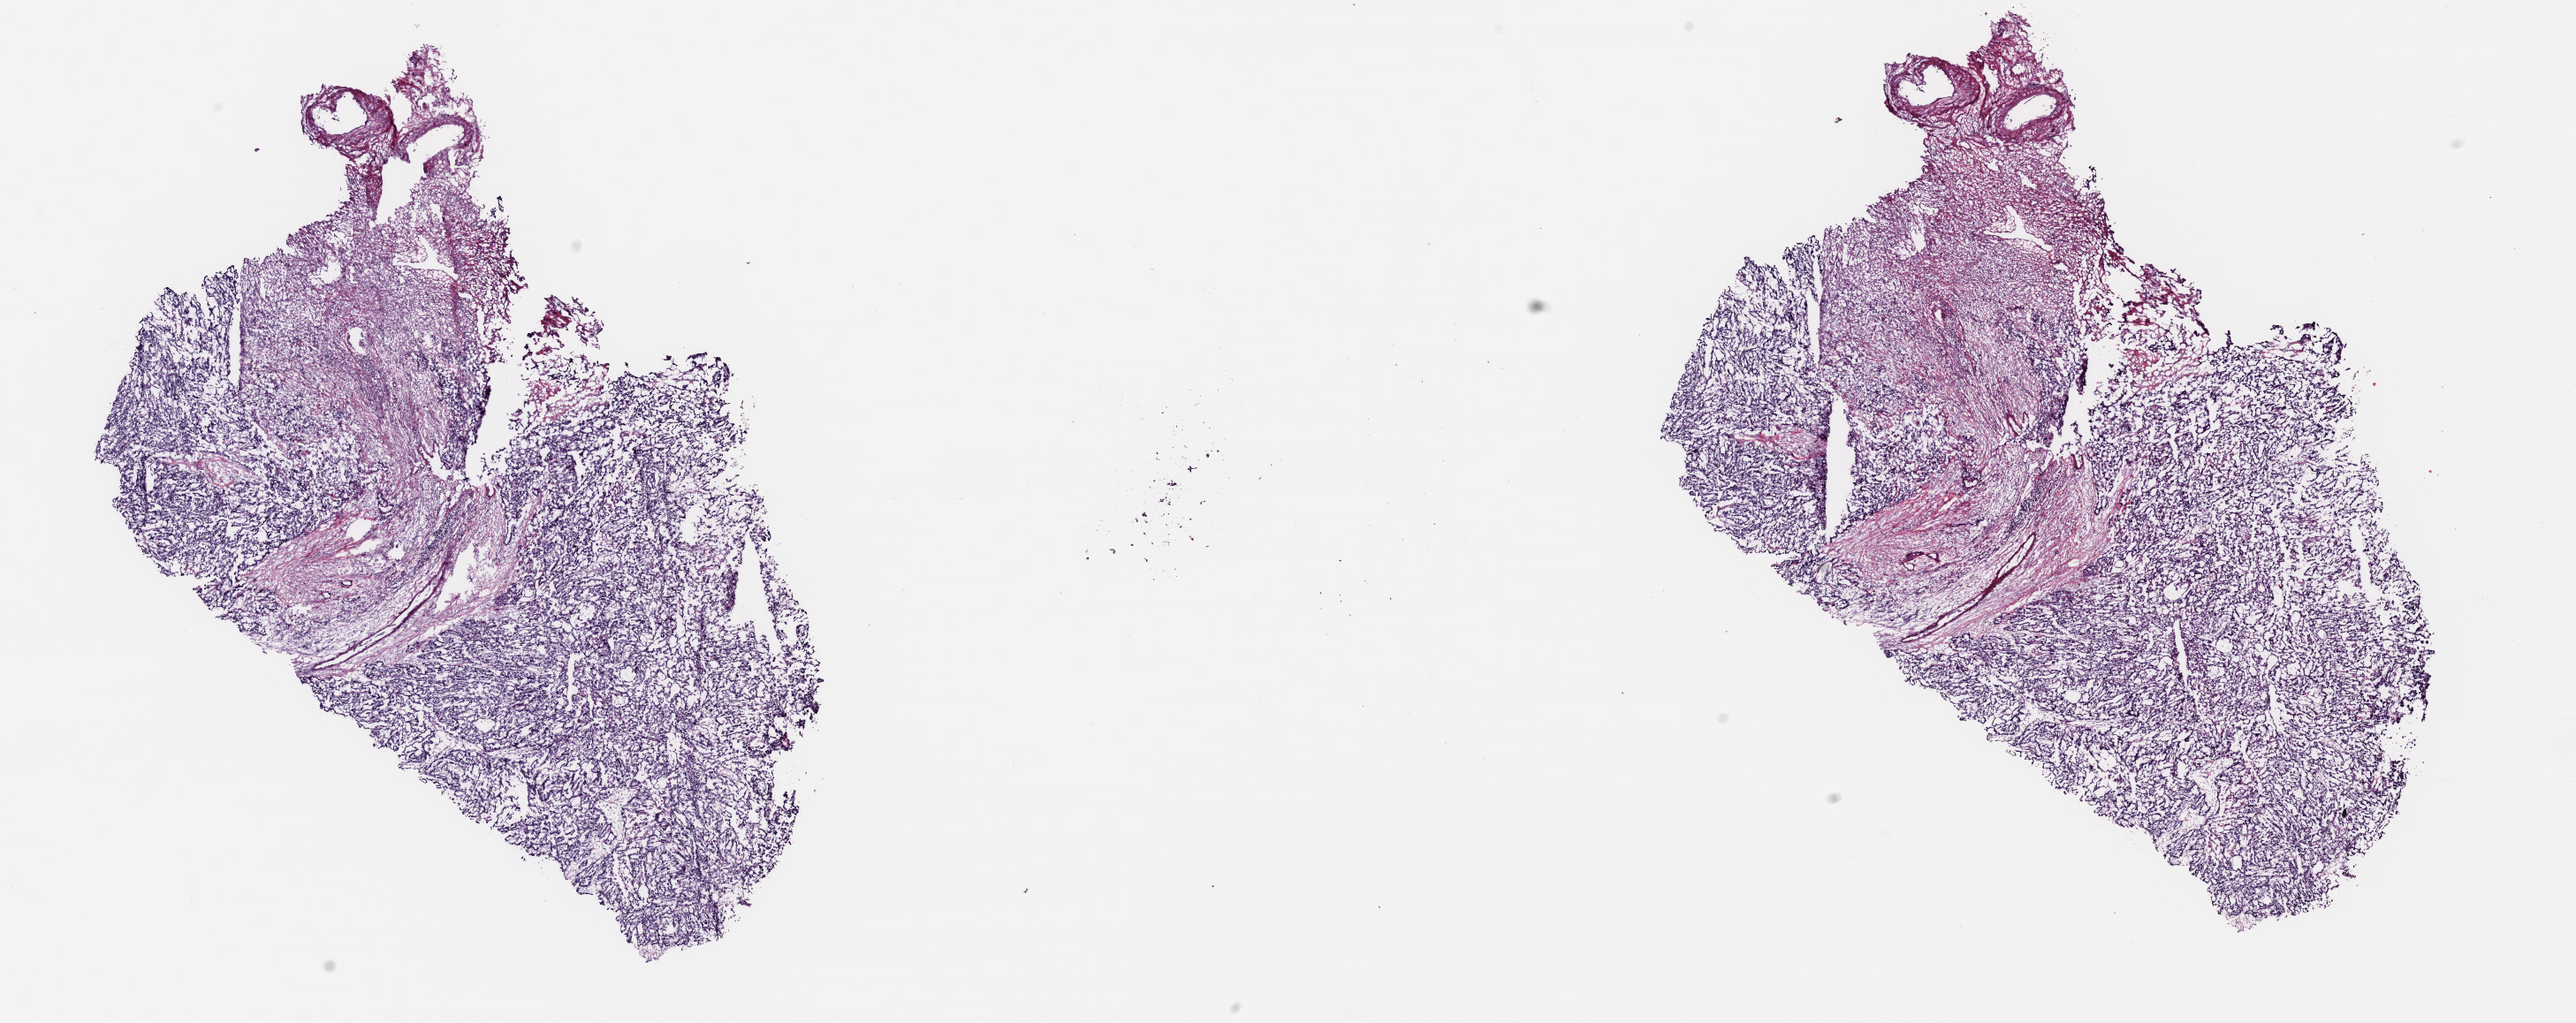
Digitized Hematoxylin and eosin (H&E) stained tissue section (whole slide) — shown as a low-resolution overview of the whole scanned area (about 23.0 x 9.1 mm), frozen section from the top of the tissue portion, uterus, primary tumour sample. Patient: female, age at initial diagnosis 51 years. Histologic grade: G3 (poorly differentiated). Pathologist review of this section (percent, as recorded): tumour cells 60%, tumour nuclei 60%, normal cells 0%, stromal cells 40%, necrosis 0%. Infiltration values recorded for this section: lymphocyte infiltration 20%, monocyte infiltration 5%, neutrophil infiltration 5%.
* FIGO stage: IIIC
* diagnosis: Serous cystadenocarcinoma, NOS (endometrium)